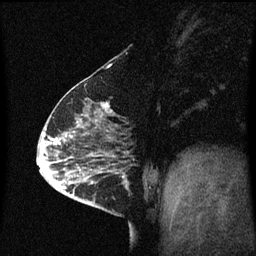
Breast MRI (dynamic contrast-enhanced), one sagittal slice; slice 21 of 60 in the series (ordered by position); dynamic contrast-enhanced series, image 2 of 3 at this slice position (ordered by acquisition); 1.5 T; TE 4.2 ms, TR 8.4 ms; 256 × 256 image matrix. Patient: female, 63 years.
Structures marked on this image (semi-automatically segmented with operator editing):
- analysis volume of interest (the breast-tissue region the enhancement analysis was run in; not a lesion): bounding box (x1, y1, x2, y2) in pixels: (98, 168, 129, 217)
- tumour enhancement mask (voxels above the 70 % enhancement threshold inside the analysis volume of interest): (102, 168, 127, 189)